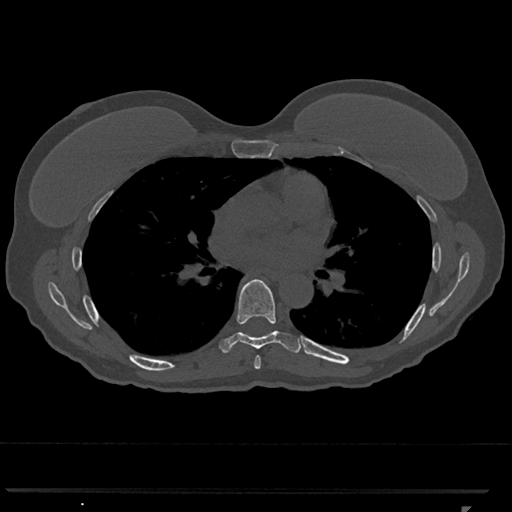
CT including the spine, one axial slice; slice 715 of 793 in the series (ordered by position); 120 kVp; bone window (W 1800 / L 400 HU); 512 × 512 image matrix, field of view 380 × 380 mm. Patient: female, 62 years. From the clinical record (not read from this slice): primary cancer: renal.
Outlined on this slice (semi-automatic segmentation, software-assisted and operator-edited):
- T6 vertebra: box from (x=254, y=356) to (x=261, y=369) px
- T7 vertebra: (x=219, y=279)–(x=302, y=353)